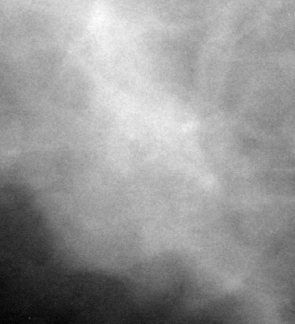
Region of interest cut from a scanned film mammogram (one marked finding); right breast; MLO view.
Marked abnormality: mass, shape irregular, margins ill defined / spiculated; BI-RADS assessment category 4; subtlety rating 3 on a 1 (subtle) to 5 (obvious) scale; pathology (as recorded): benign.